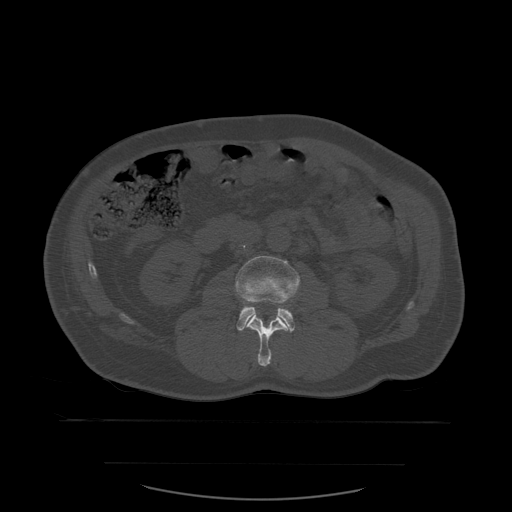
CT including the spine, one axial slice. Slice 204 of 590 in the series (ordered by position). Bone window (W 1800 / L 400 HU). 512 × 512 image matrix. Patient age 71 years. From the clinical record (not read from this slice): primary cancer: lung.
Annotated regions visible in this slice (semi-automatic segmentation, software-assisted and operator-edited):
- L2 vertebra: box from (x=246, y=311) to (x=292, y=367) px
- L3 vertebra: (x=235, y=256)–(x=301, y=332)